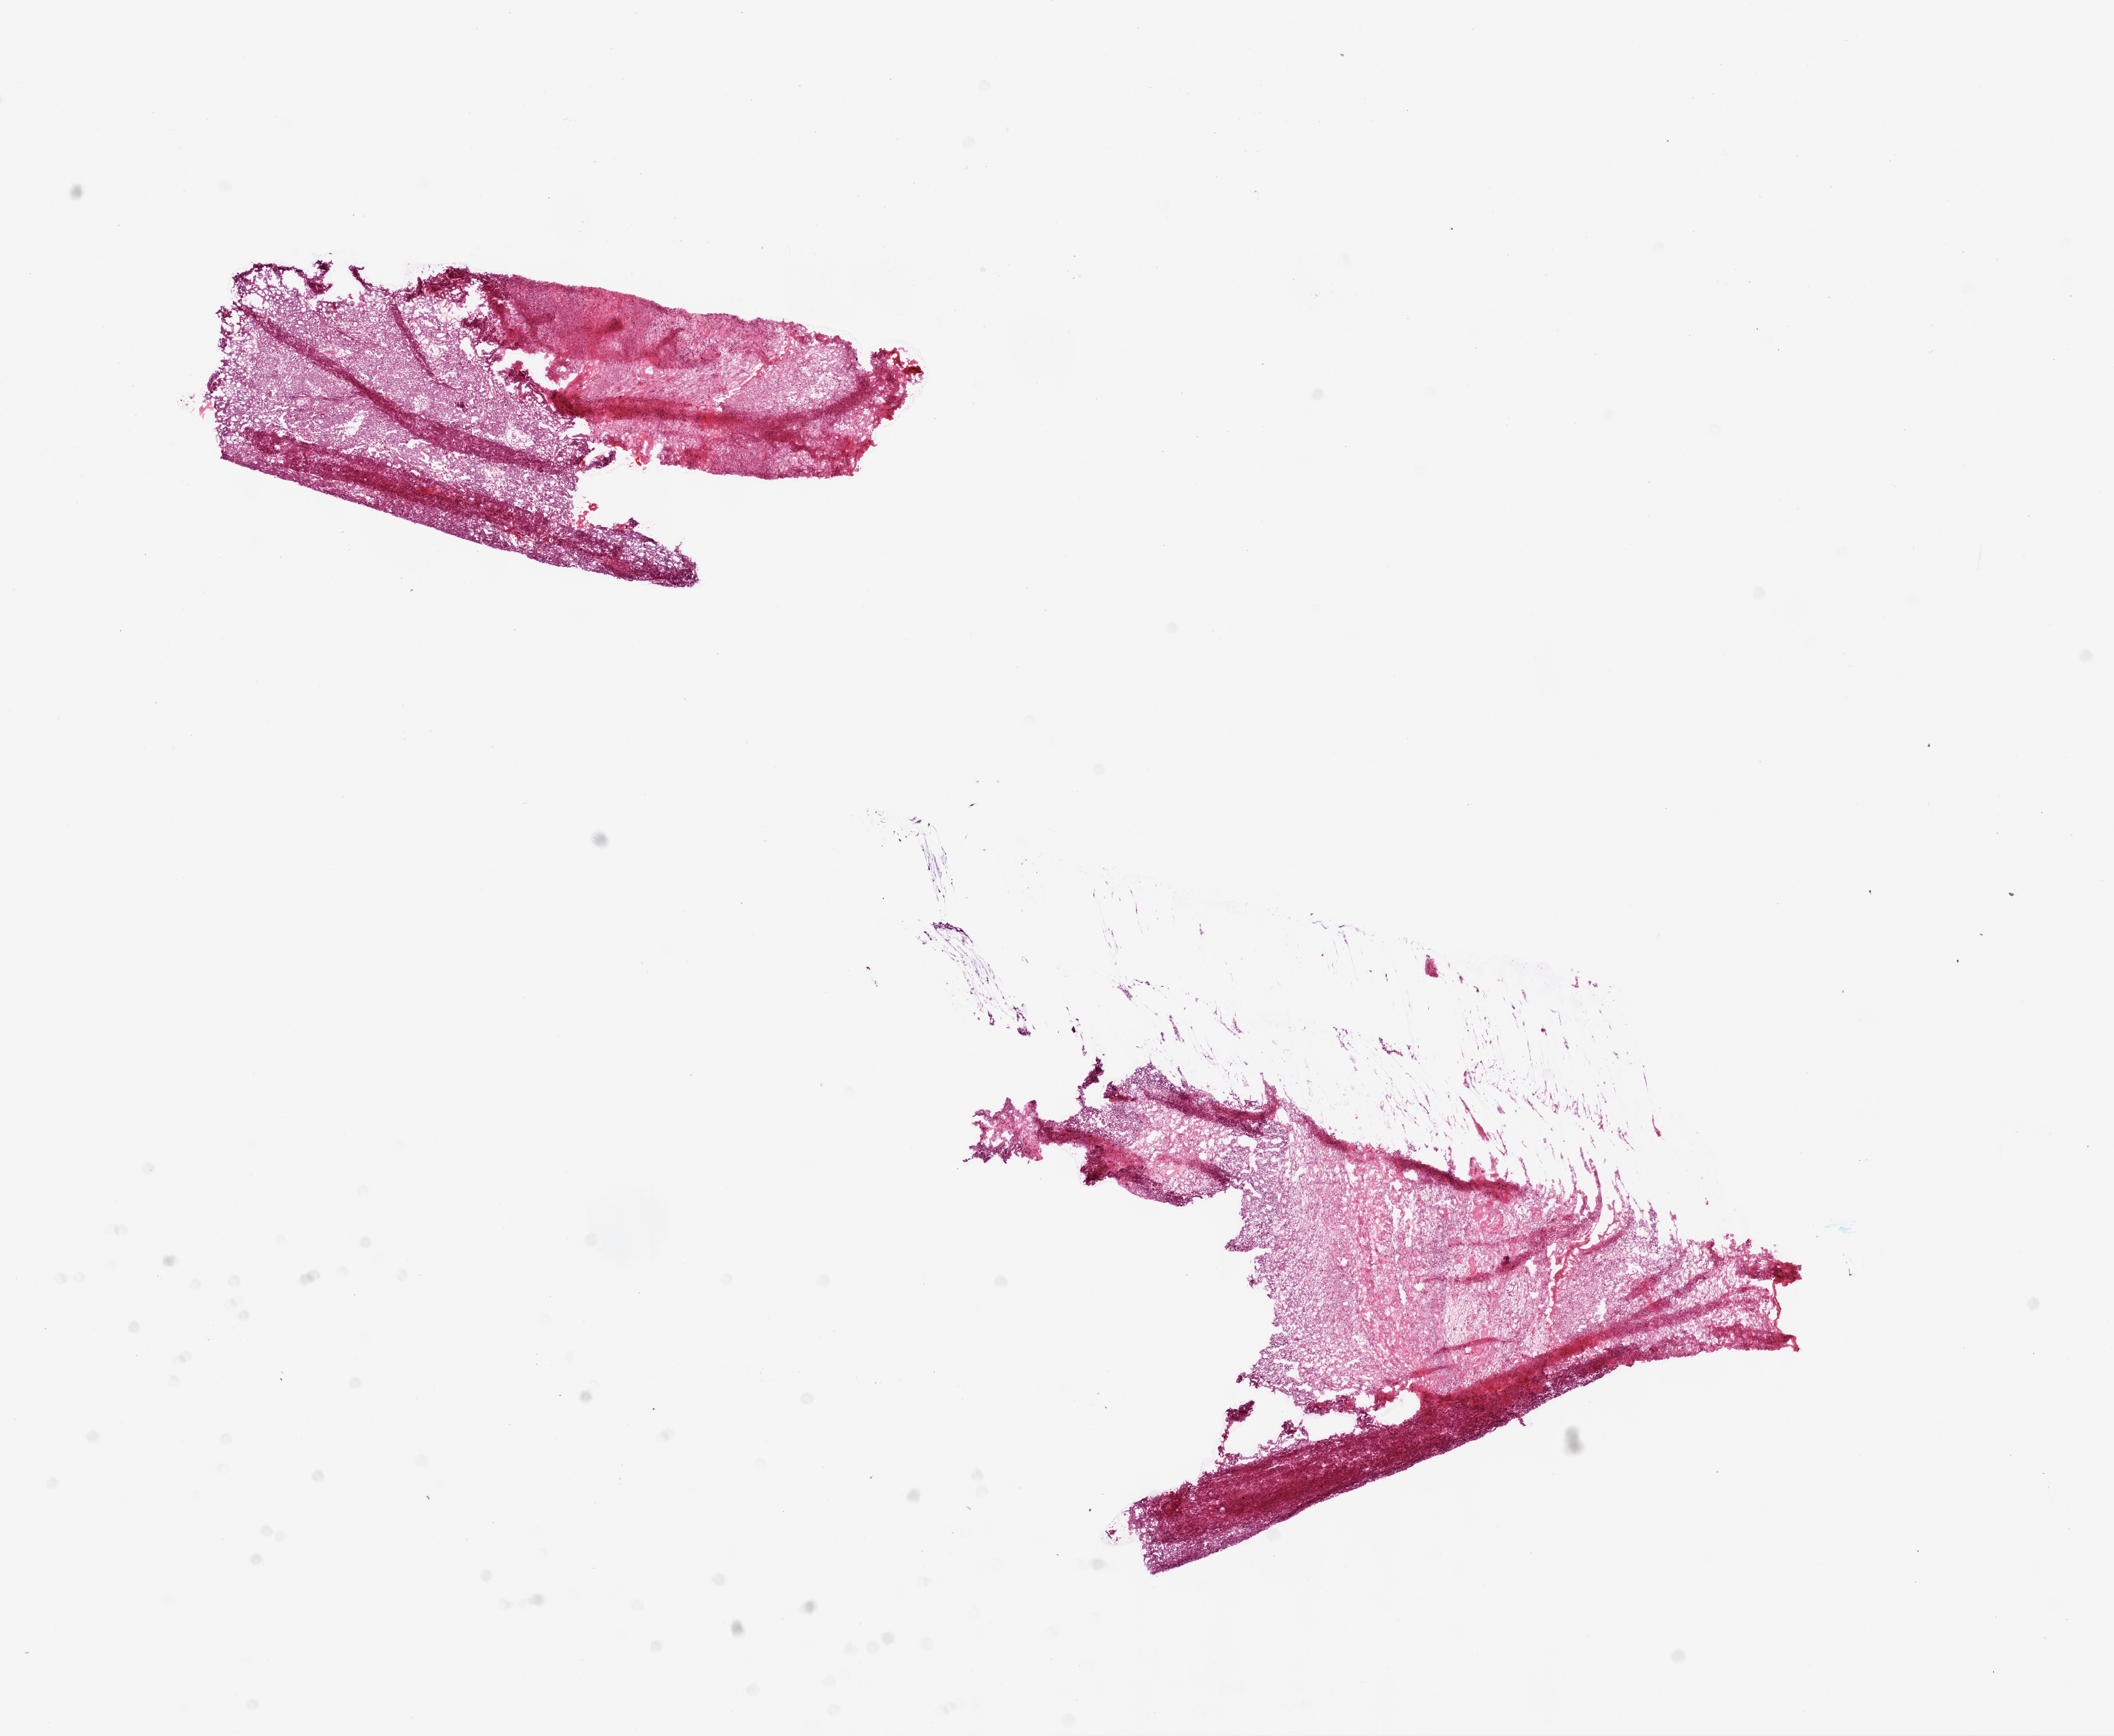
Digitized H&E-stained tissue section (whole slide), whole scanned area (about 12.6 x 10.3 mm) shown as a low-resolution overview; frozen section from the top of the tissue portion; ovary, primary tumour sample. Female, age 65 years at initial diagnosis. Histologic grade: G3 (poorly differentiated). Composition of this section per pathologist review: tumour cells 85%, tumour nuclei 85%, normal cells 10%, stromal cells 5%, necrosis 0%.
FIGO stage: IIIC. Pathologic diagnosis: Serous cystadenocarcinoma, NOS.